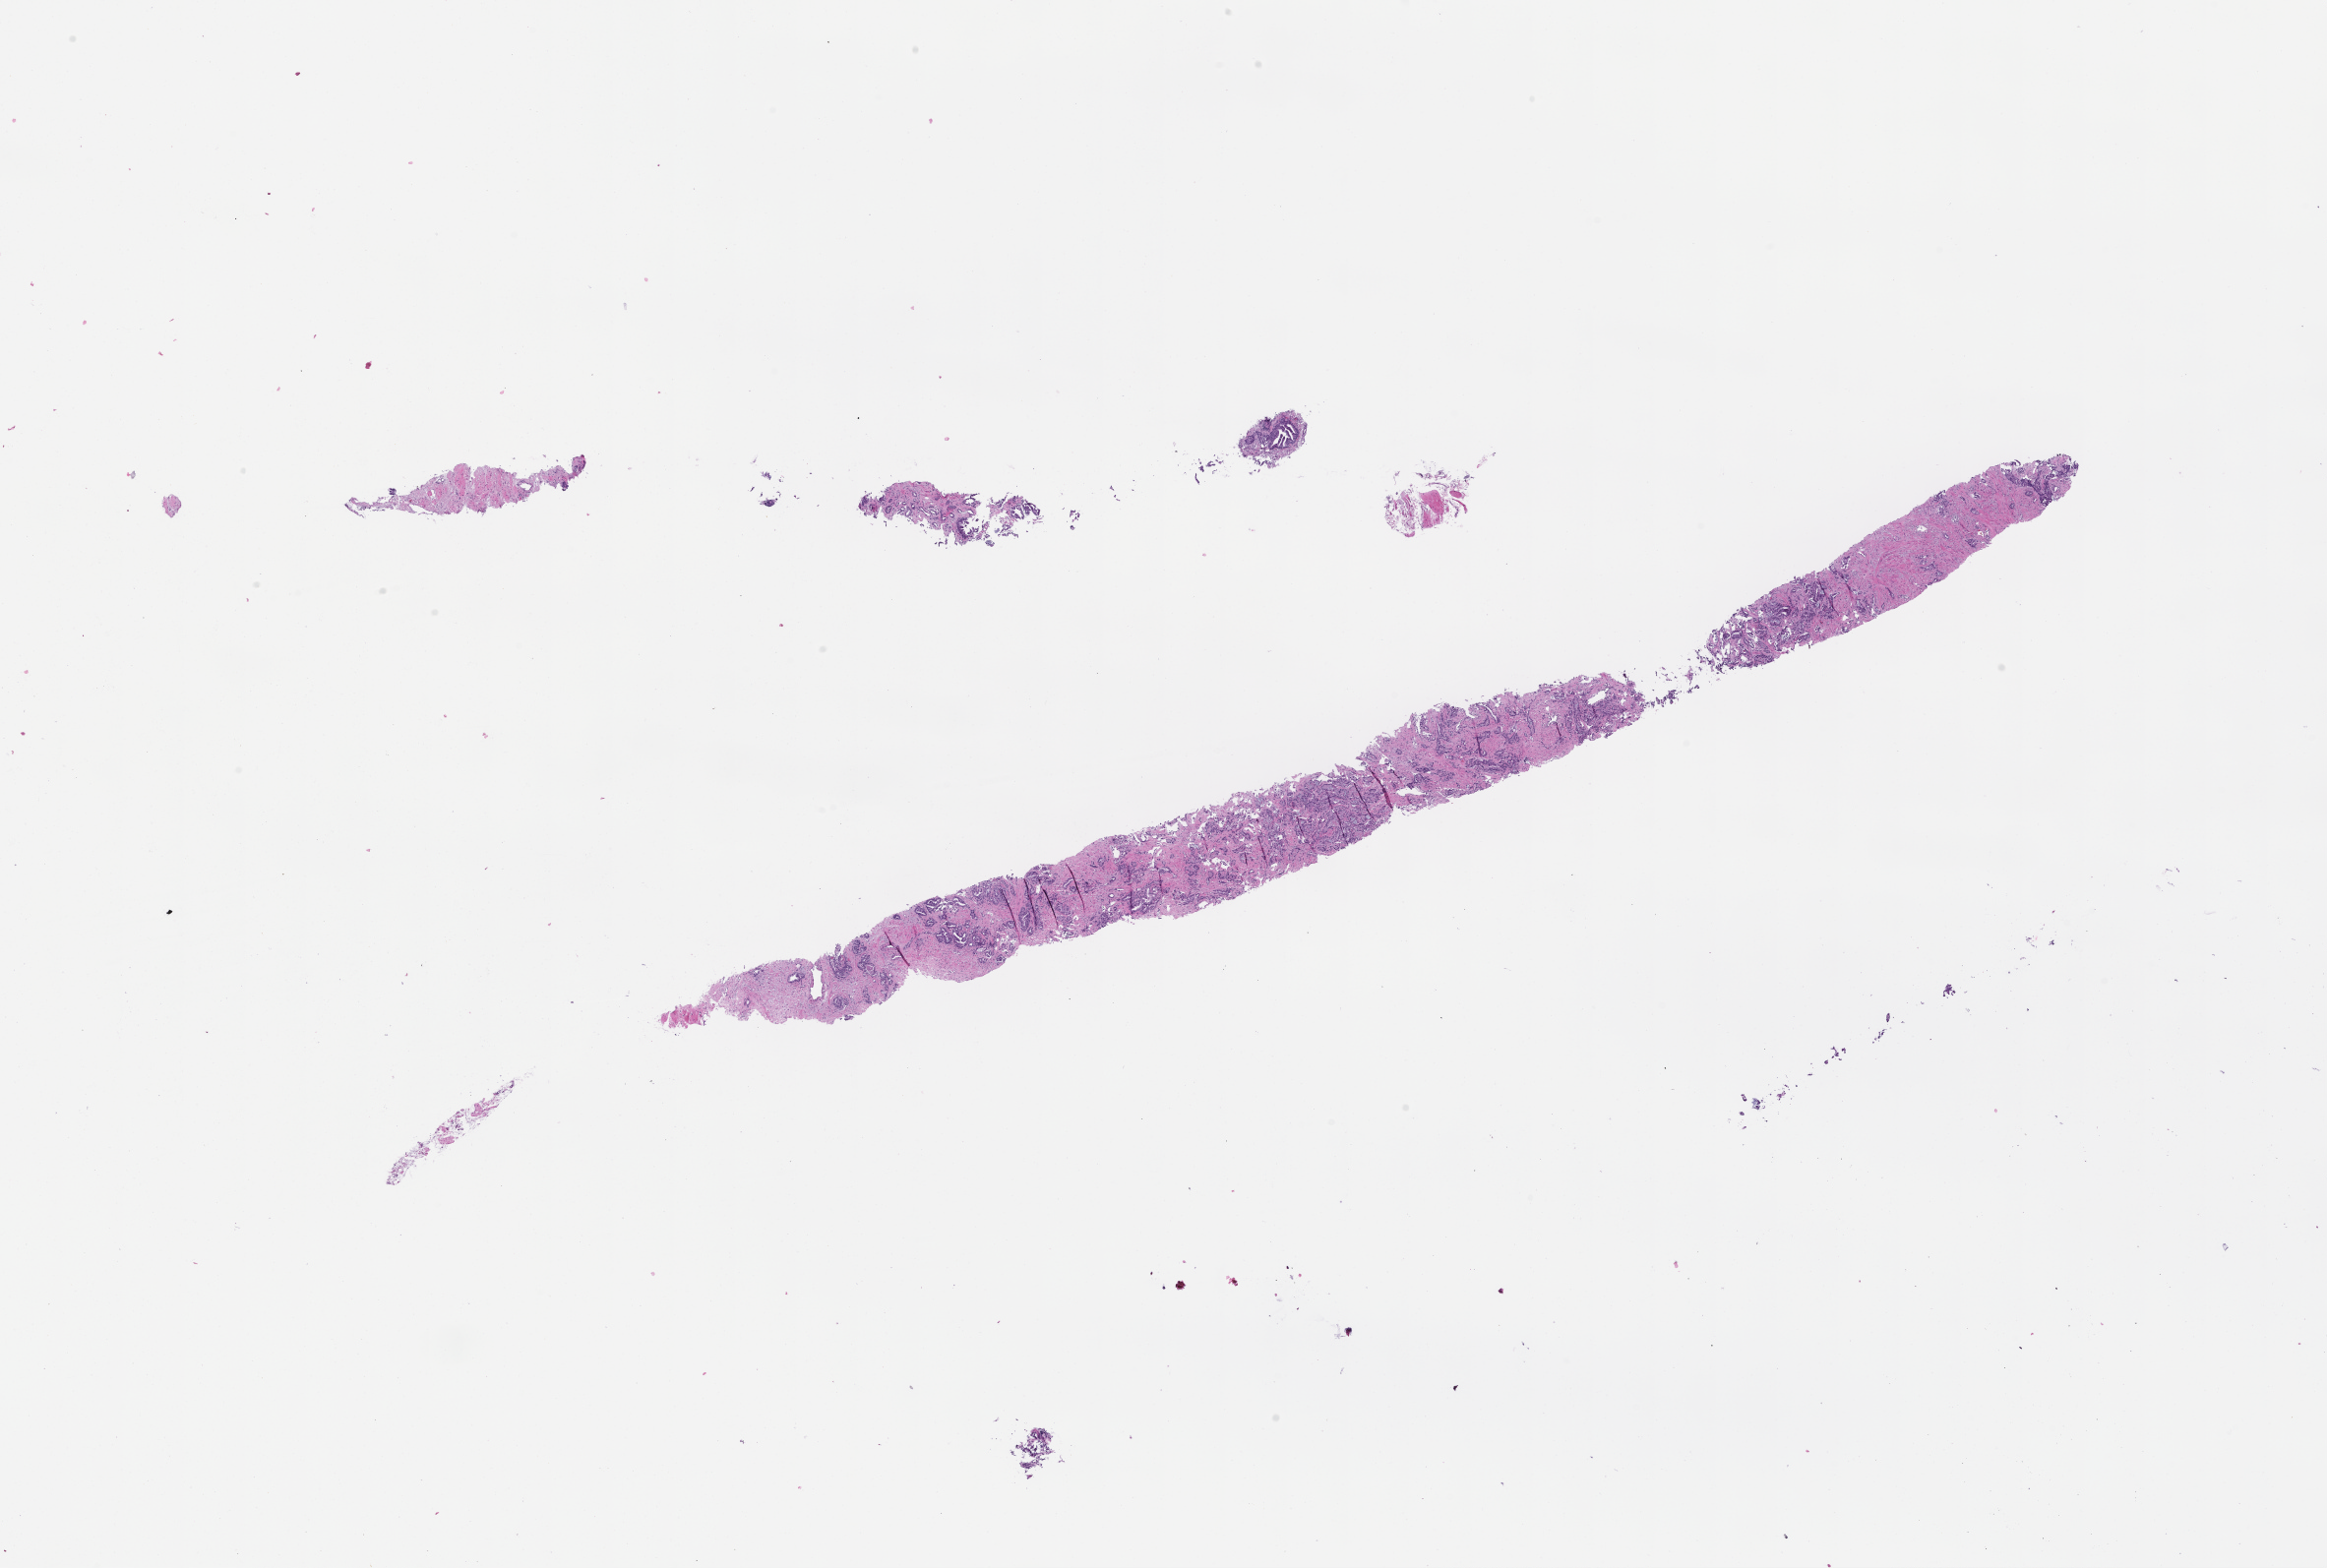
Whole-slide image, H&E stain, whole scanned area (about 19.1 x 12.9 mm) shown as a low-resolution overview; FFPE section; site: prostate. Patient sex: male.
• this section: primary tumour tissue
• diagnosis: Prostate Carcinoma